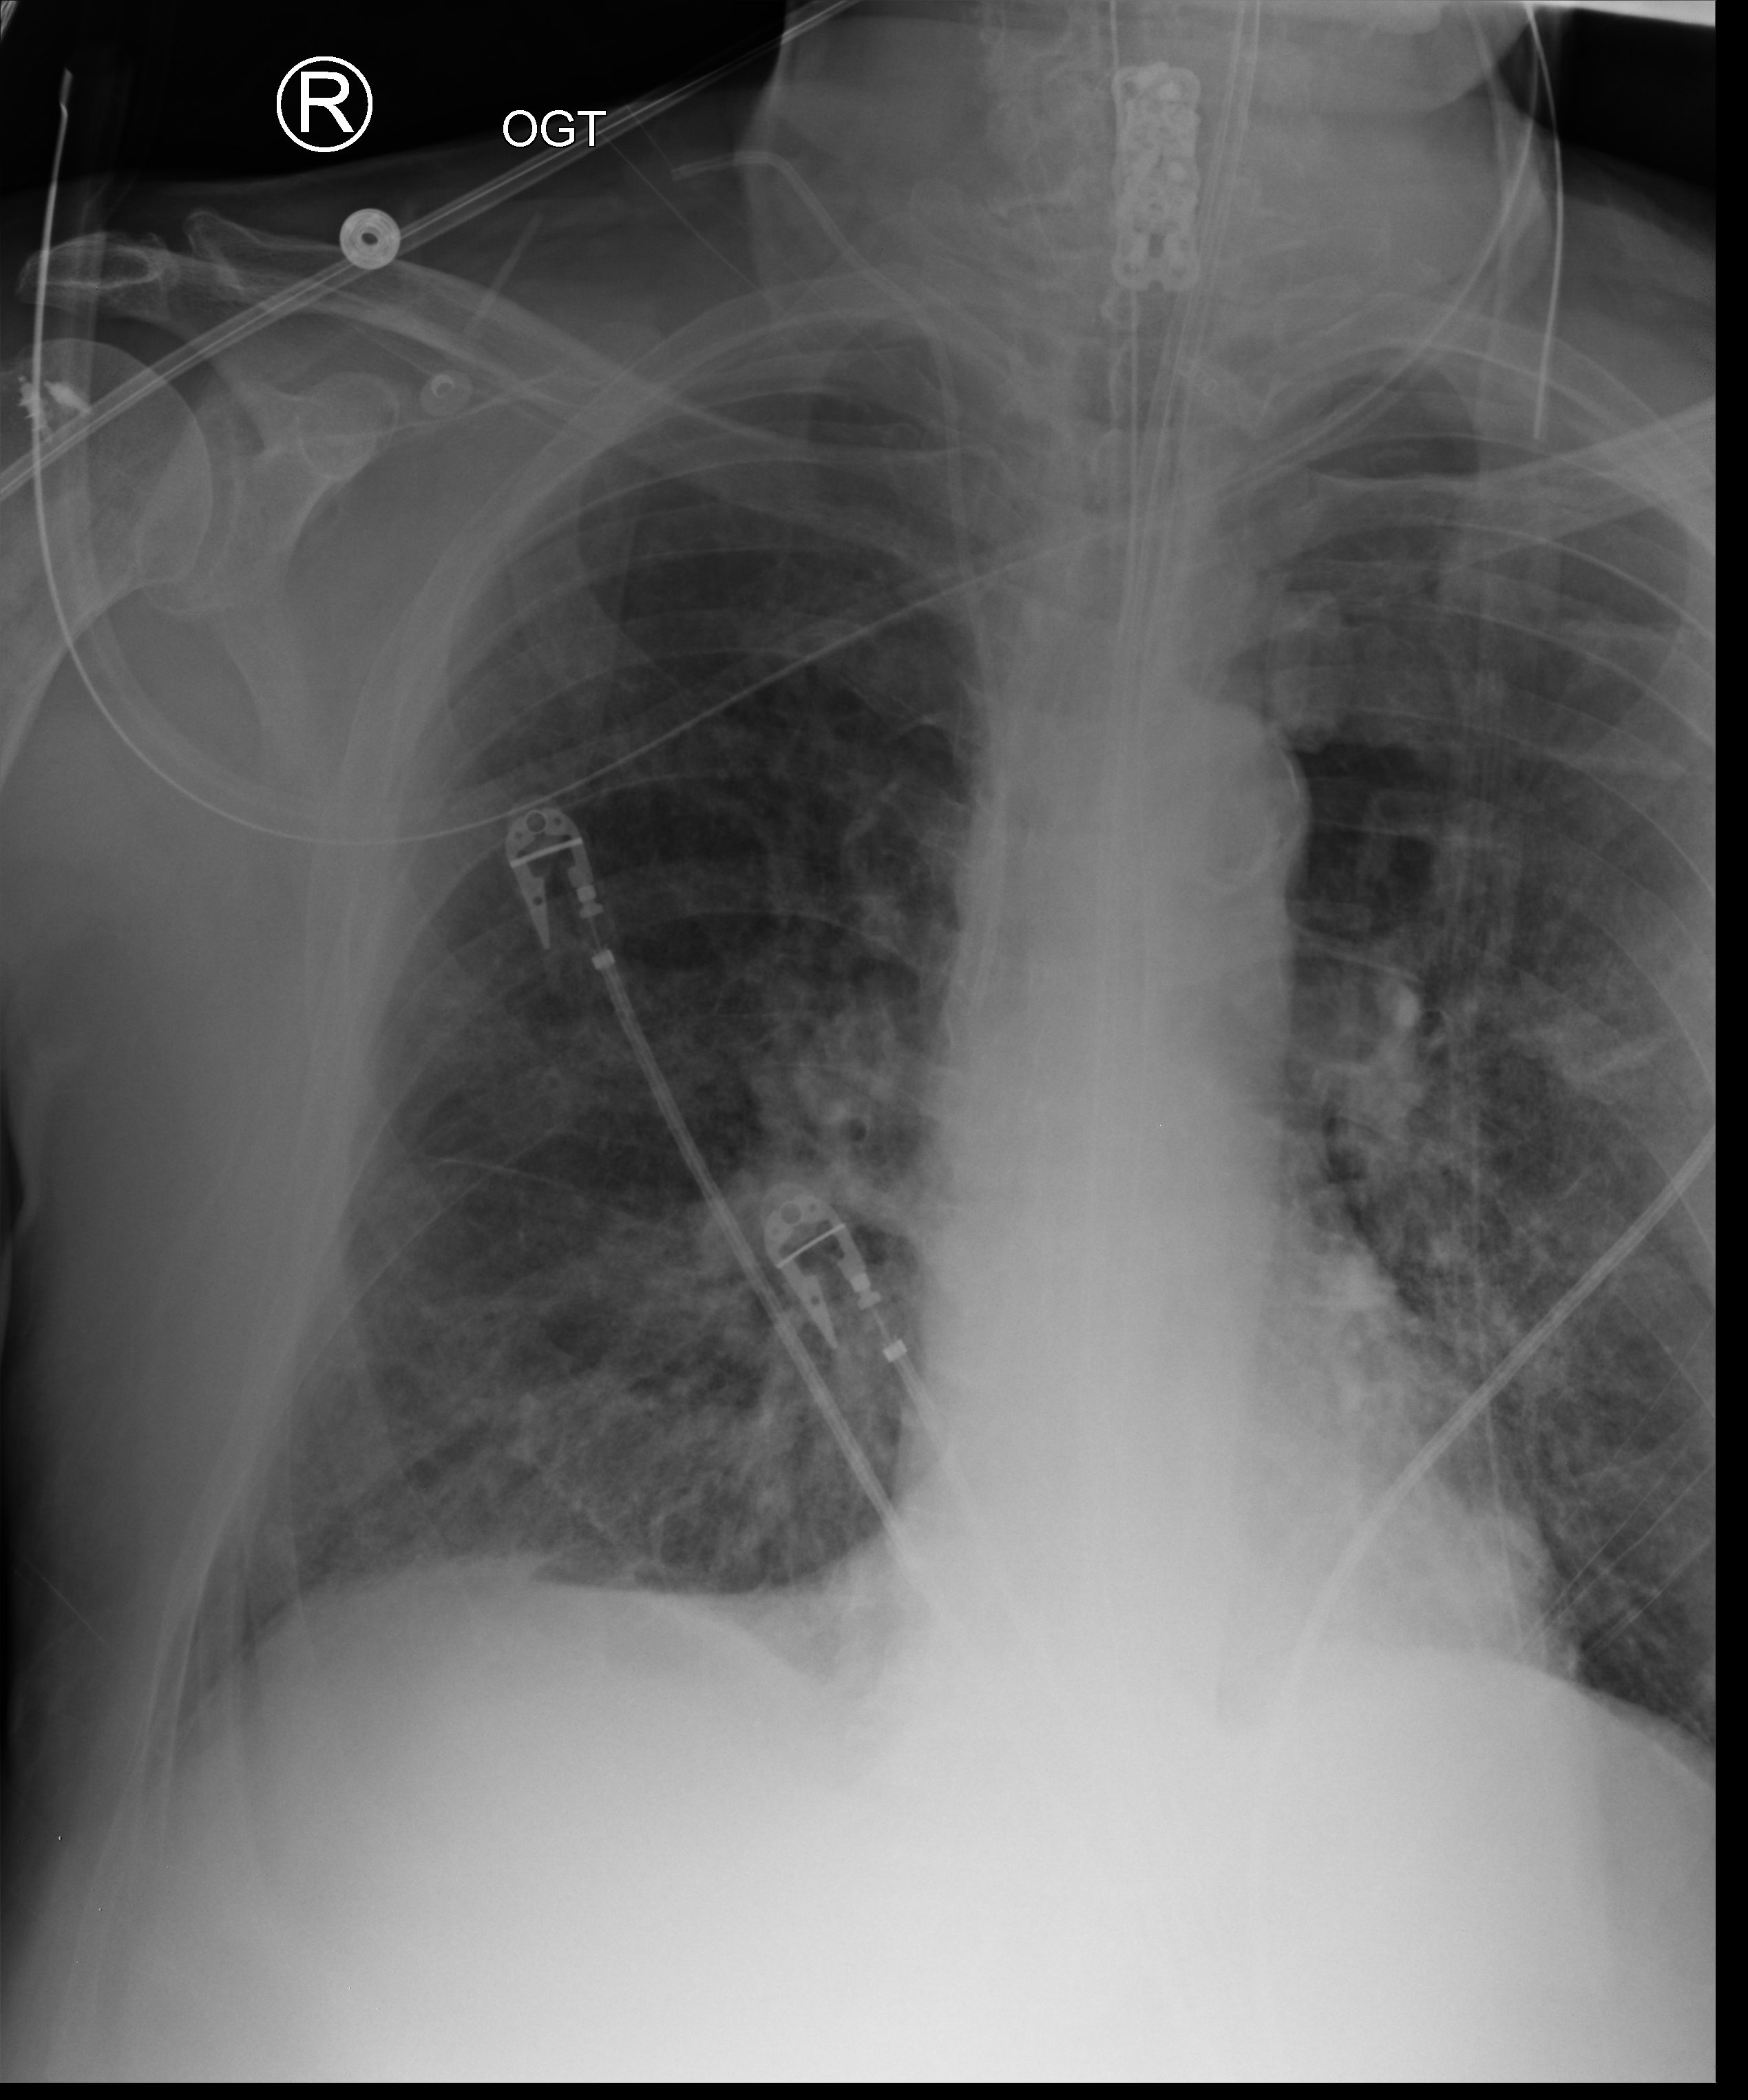
Chest X-ray (portable). Patient hospitalised with COVID-19; male, aged 75–90 years.
From the hospital-stay record, not from the radiograph (when in the stay this image was taken is not recorded): smoking status (admission record): former.